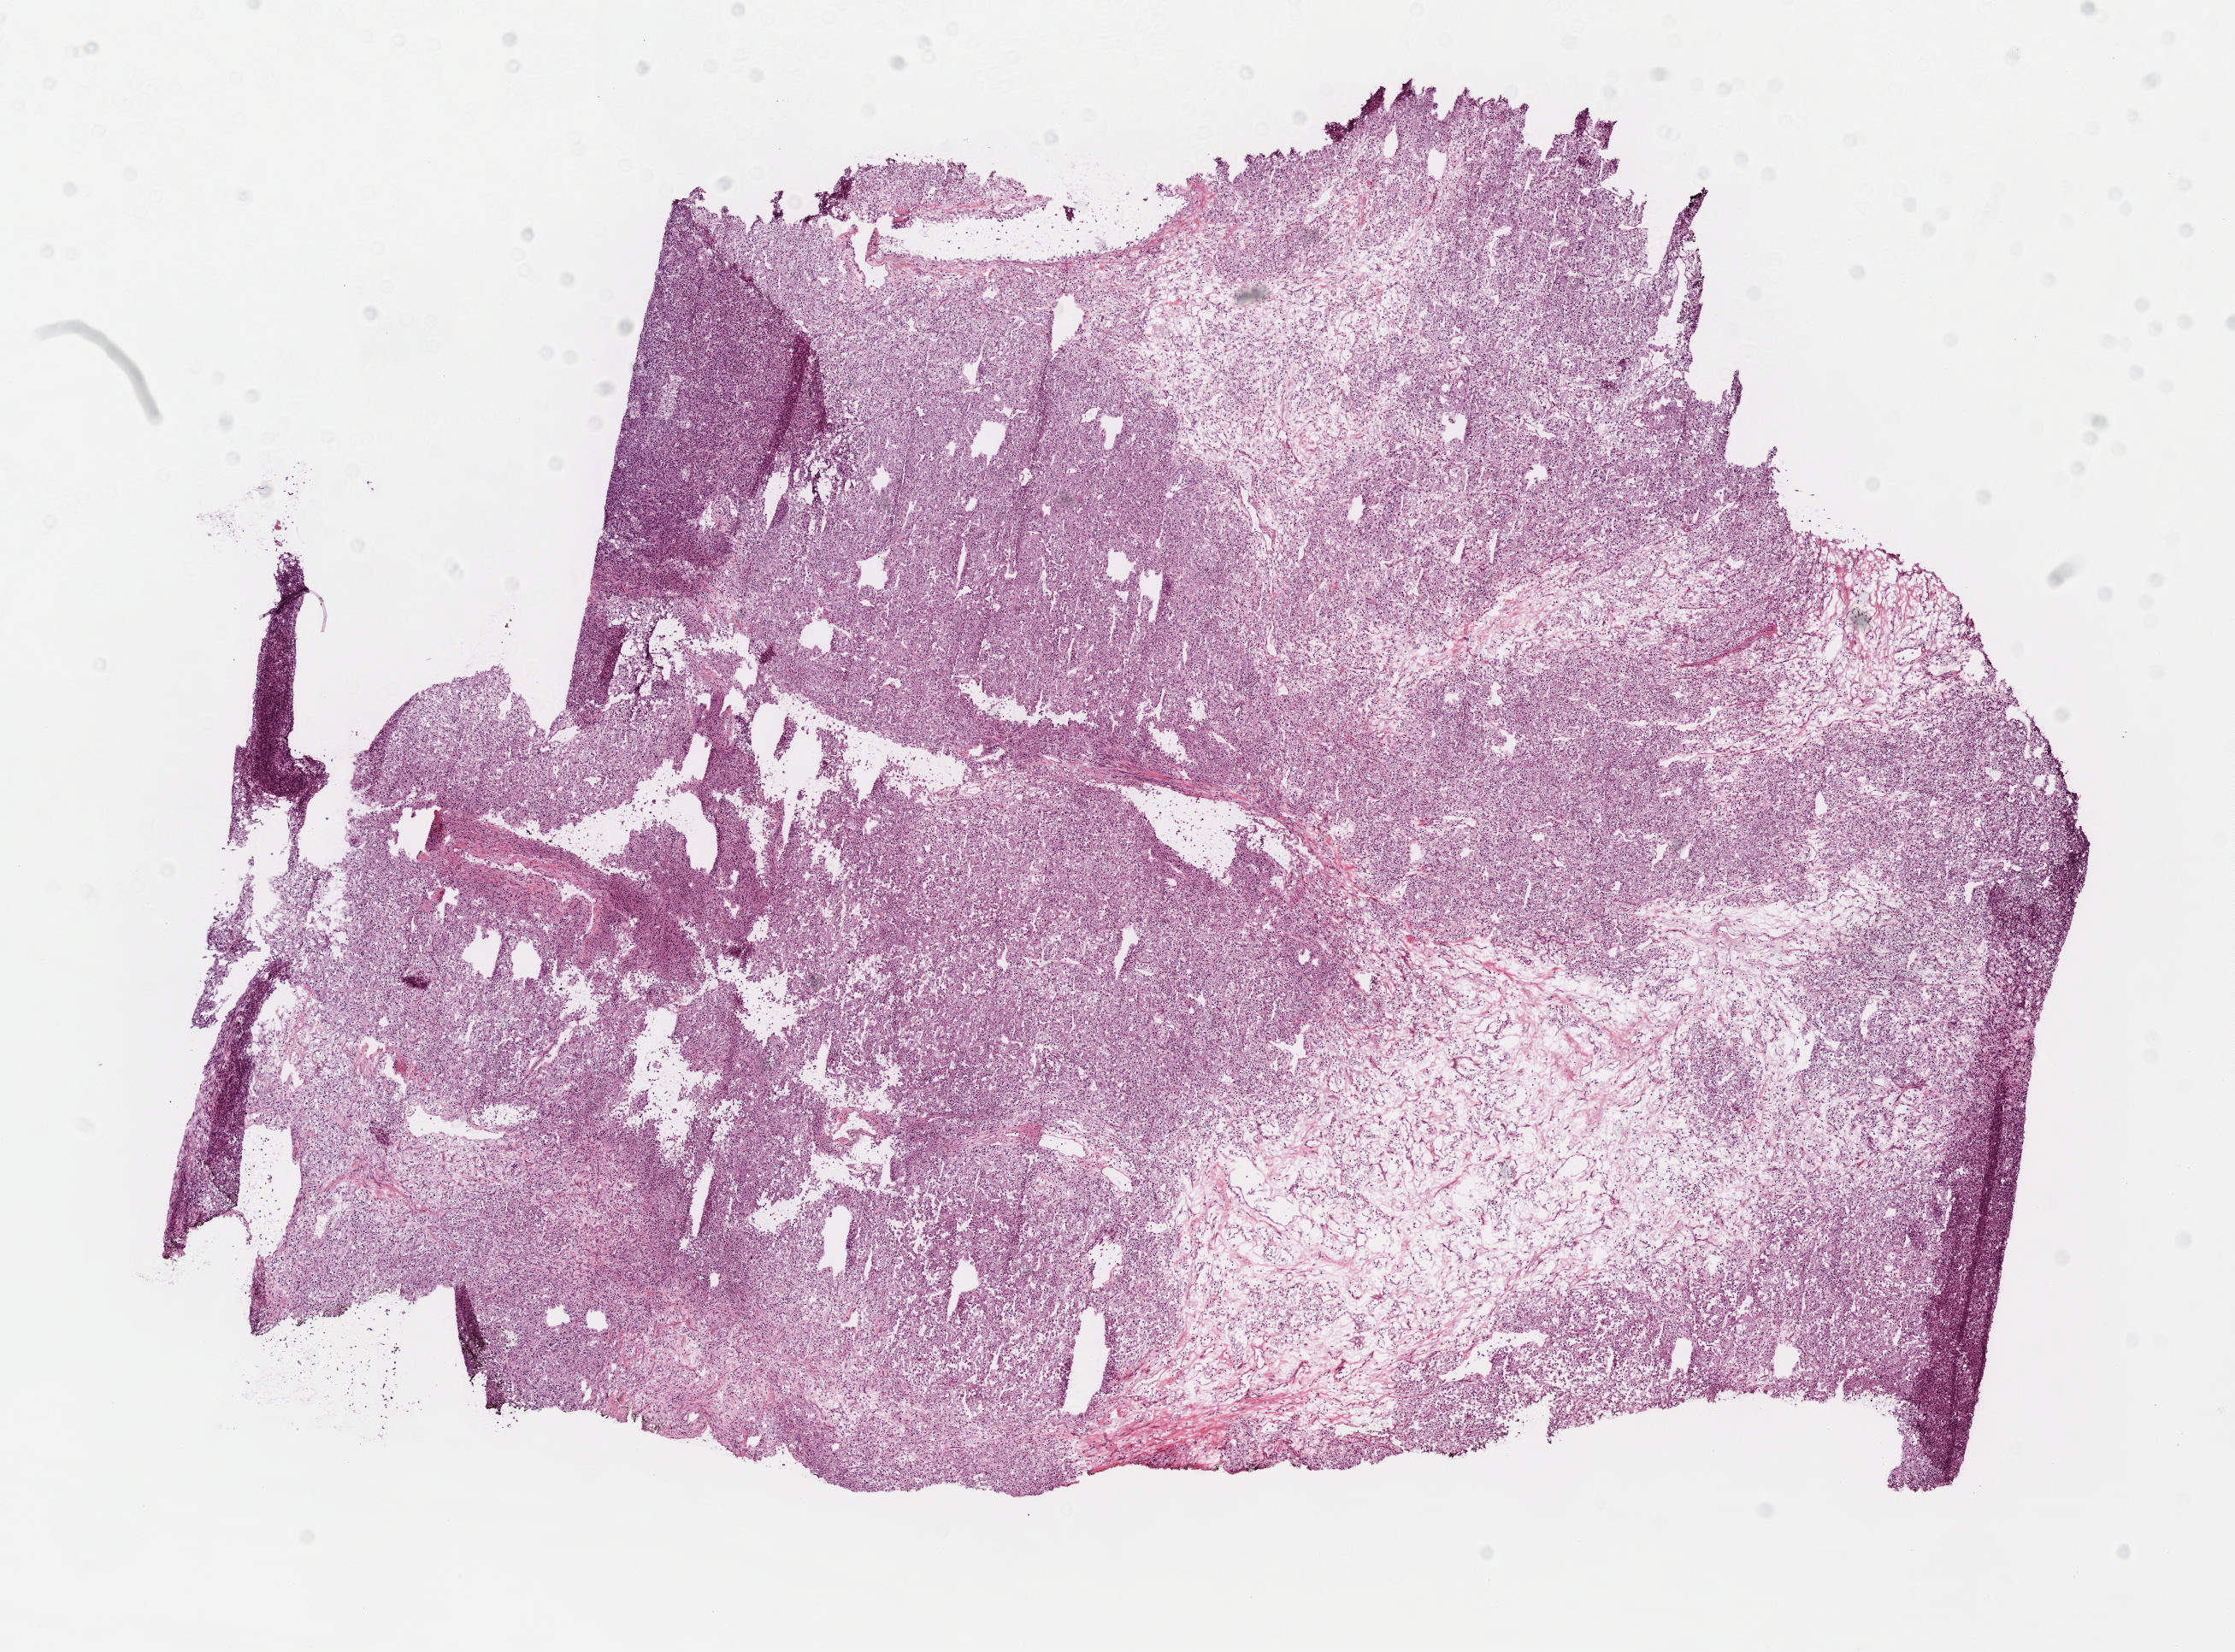
Digitized Hematoxylin and eosin (H&E) stained tissue section (whole slide) — shown as a low-resolution overview of the whole scanned area (about 10.6 x 7.8 mm), frozen section from the top of the tissue portion, sample: primary tumour, kidney. Patient: male, age at initial diagnosis 46 years. Histologic grade: G3 (poorly differentiated). Composition of this section per pathologist review: tumour cells 85%, tumour nuclei 85%, normal cells 0%, stromal cells 15%, necrosis 0%.
Diagnosis: Clear cell adenocarcinoma, NOS. Laterality: left. AJCC pathologic stage: IV. TNM: T3 NX M1.